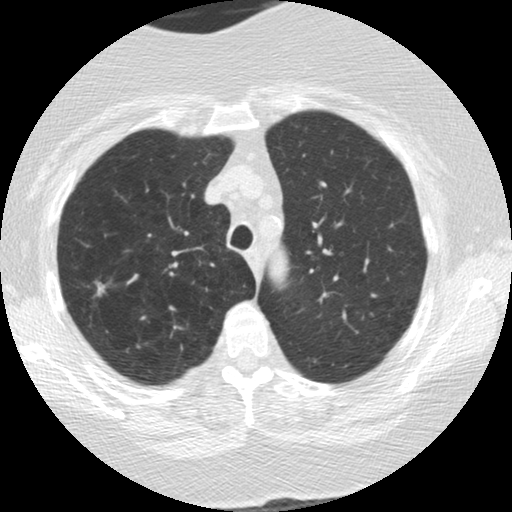
Low-dose screening chest CT, one axial slice; lung window (W 1500 / L -600 HU); 512 × 512 image matrix, field of view 309 × 309 mm.
Annotated regions visible in this slice (outlined manually by an expert reader):
- lesion 2 (tumor, upper lobe of right lung): bounding box (x1, y1, x2, y2) in pixels: (96, 282, 105, 296)